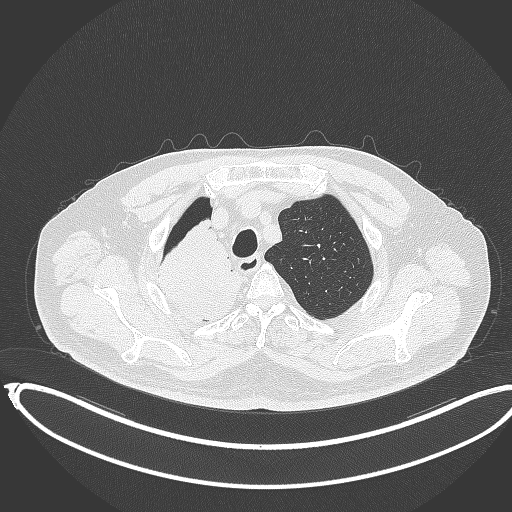
Chest CT, one axial slice; position 309 of 403 along the scan axis; reconstruction kernel B70f; 120 kVp; lung window (W 1500 / L -600 HU); 1 mm slice thickness; 512 × 512 image matrix. Patient: male, 68 years. From the clinical record (not read from this slice): clinical TNM (as recorded): T2a N0 M0.
Outlined on this slice (rectangle marked by the reading radiologist):
- lung tumour (recorded histology: adenocarcinoma): box from (x=150, y=222) to (x=243, y=324) px